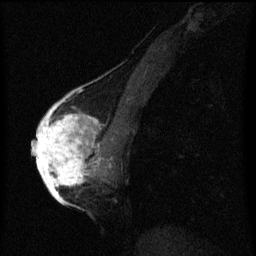
Breast MRI (dynamic contrast-enhanced), one sagittal slice; dynamic contrast-enhanced series, image 2 of 3 at this slice position (ordered by acquisition); 1.5 T; TE 4.2 ms, TR 8 ms; 2 mm slice thickness; 256 × 256 image matrix, field of view 180 × 180 mm. Patient: female, 56 years.
Annotated regions visible in this slice (semi-automatically segmented with operator editing):
- analysis volume of interest (the breast-tissue region the enhancement analysis was run in; not a lesion): box from (x=42, y=110) to (x=107, y=193) px
- tumour enhancement mask (voxels above the 70 % enhancement threshold inside the analysis volume of interest): (x=42, y=110)–(x=99, y=193)